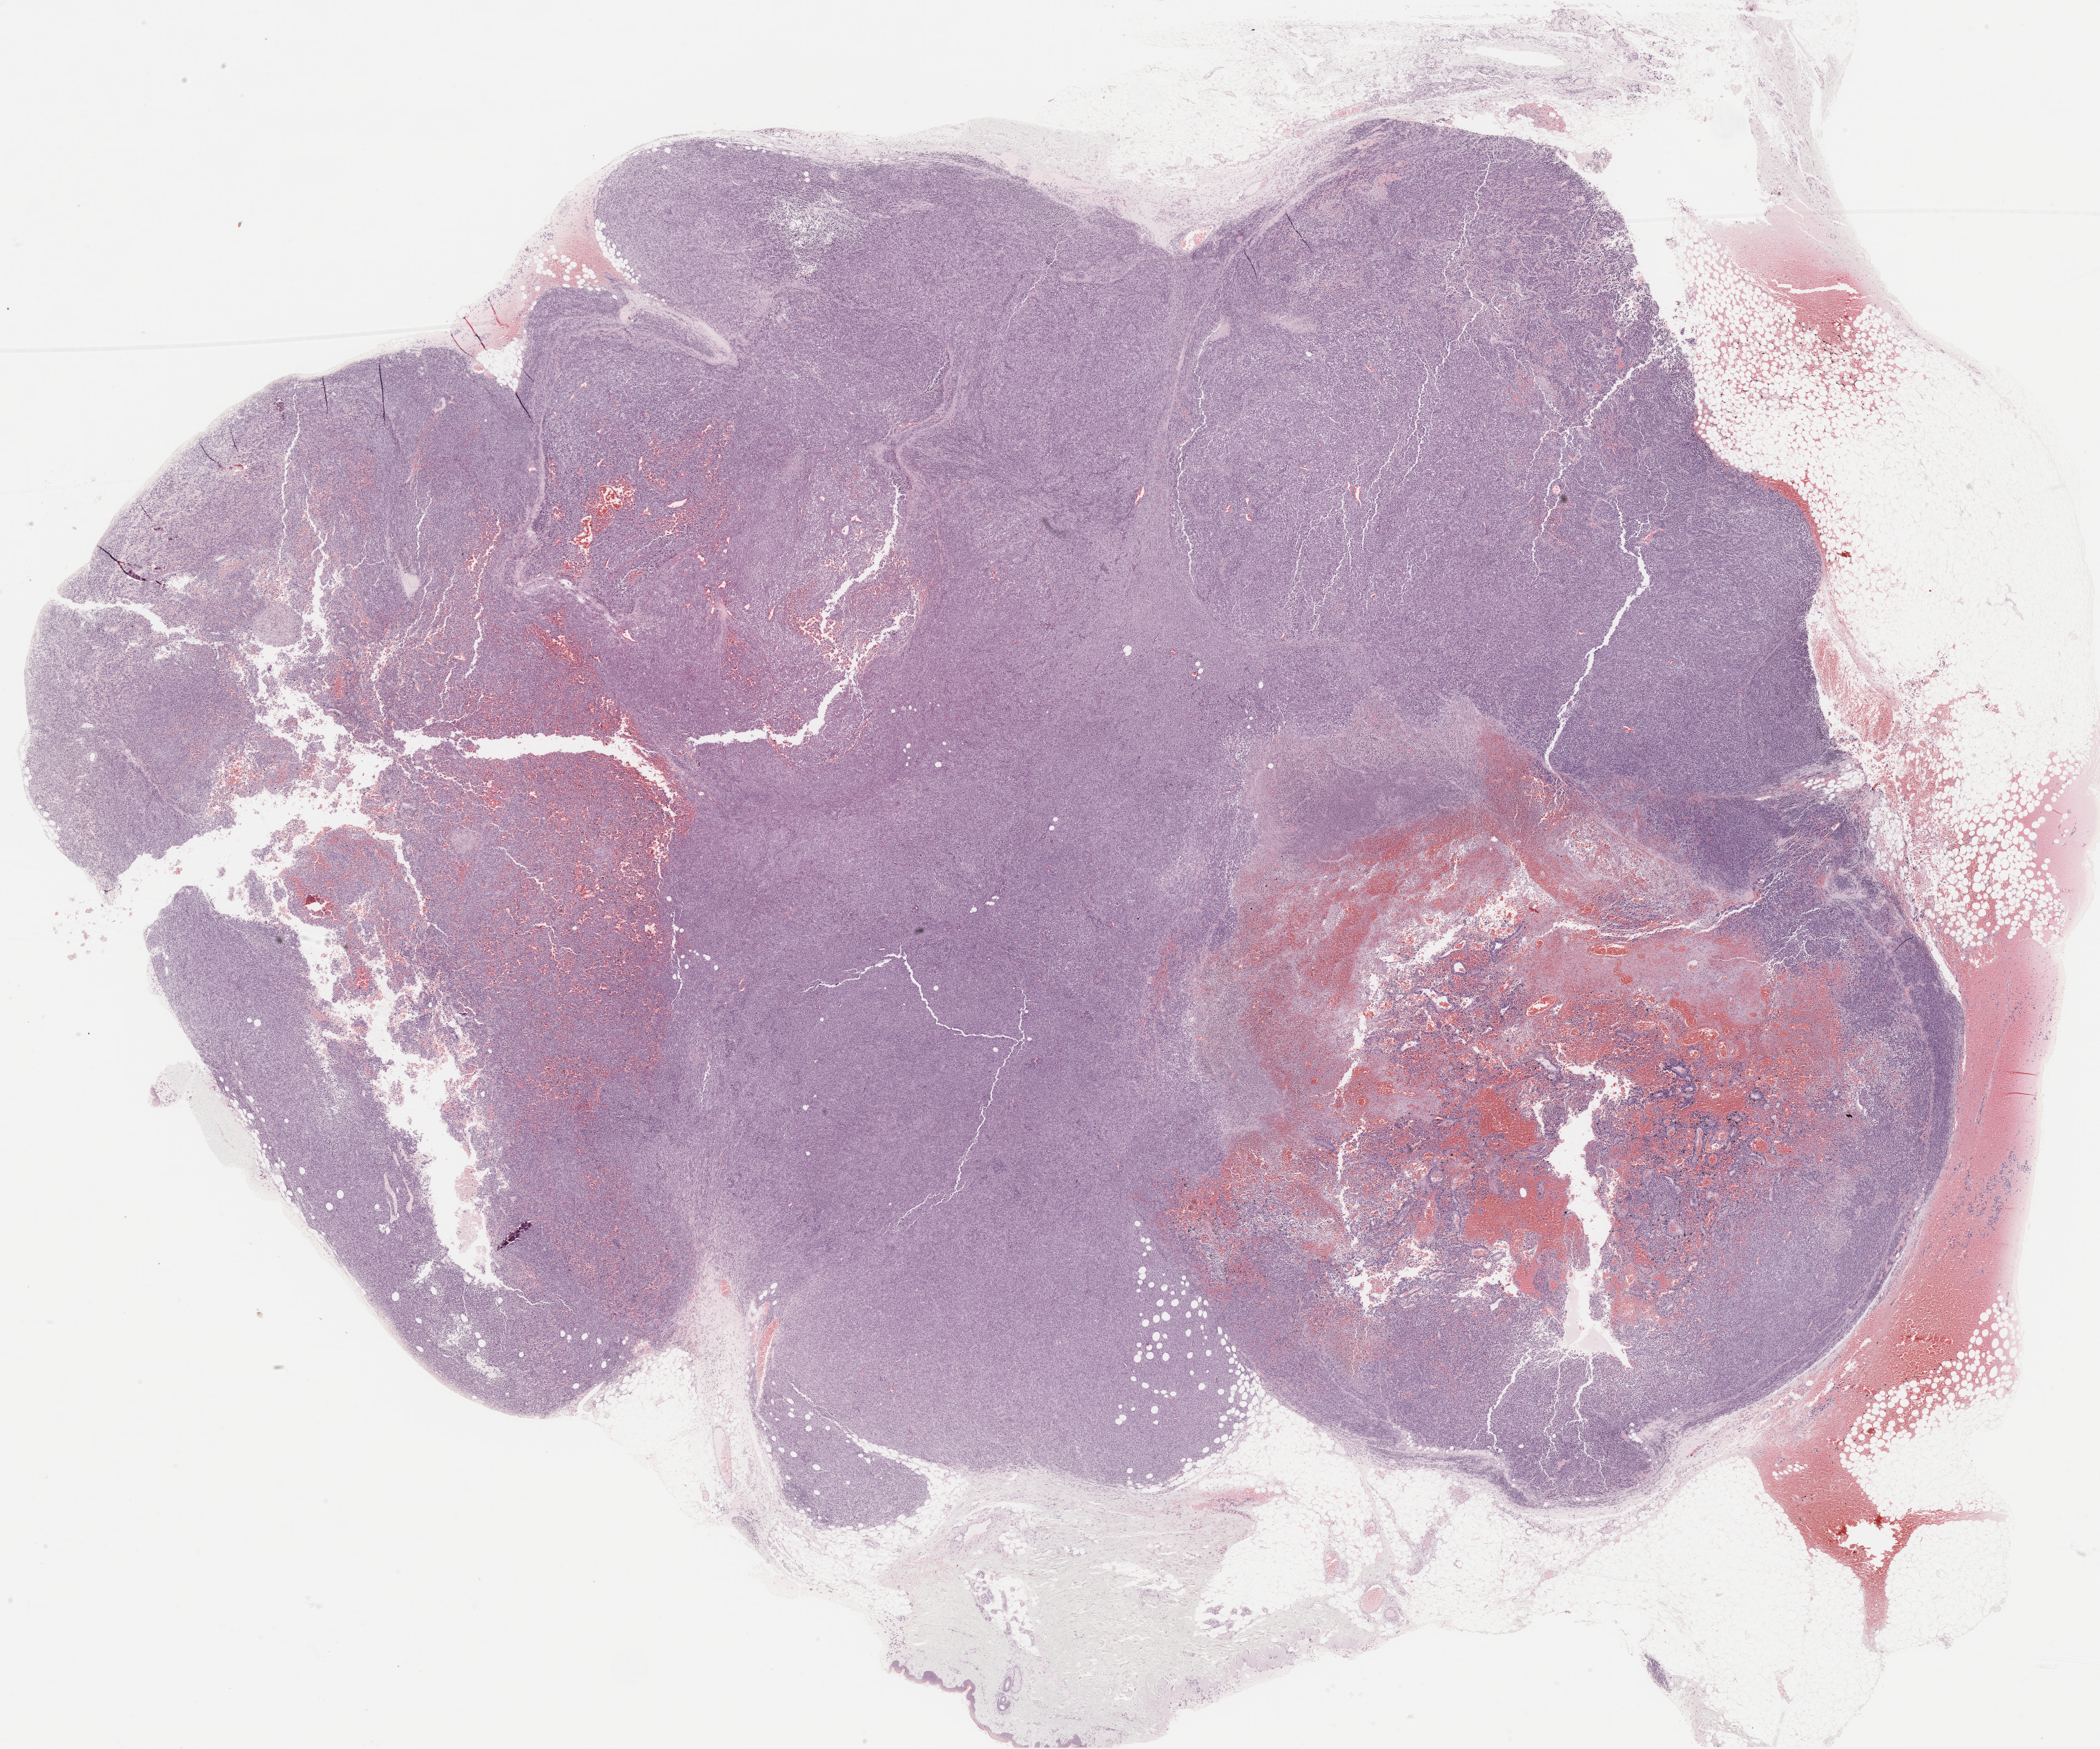
Digitized H&E-stained tissue section (whole slide), low-resolution overview of the scanned area, about 24.5 x 20.4 mm (acquisition: 20x scan); formalin-fixed paraffin-embedded (FFPE) diagnostic section; metastatic tumour sample, sampled site not recorded. Female, age 74 years at initial diagnosis.
This section: metastatic tumour tissue. Patient diagnosis: Malignant melanoma, NOS.